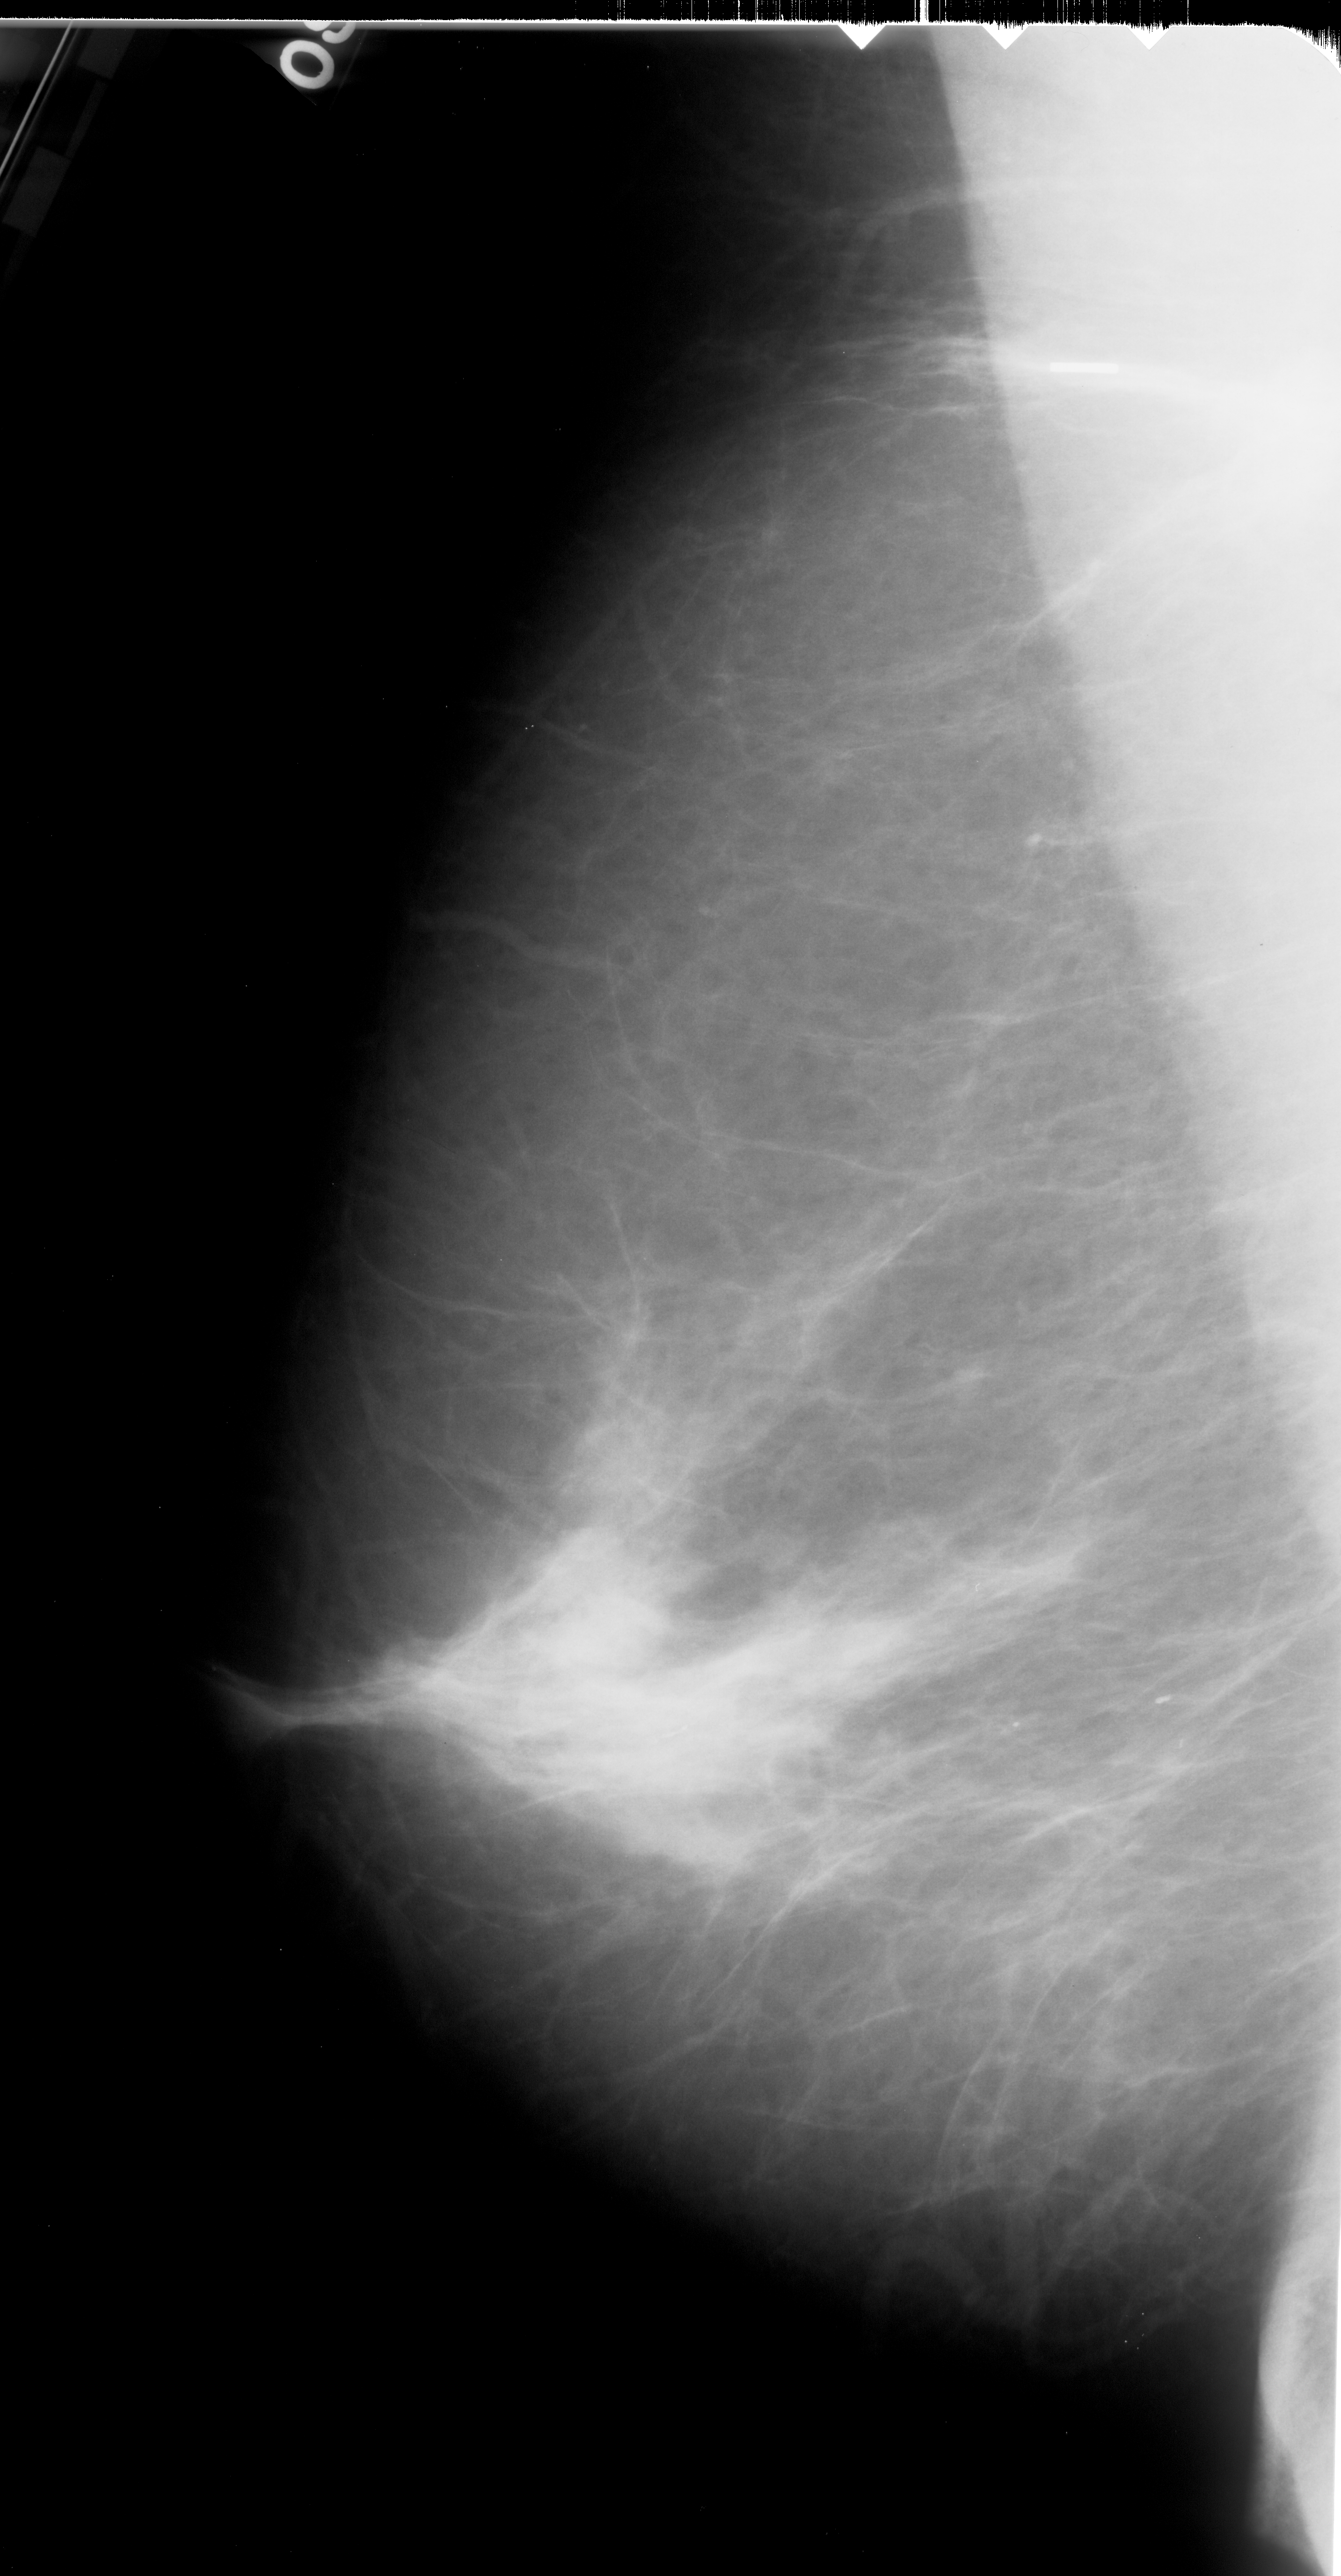
Mammogram (digitized film), left breast, MLO view, BI-RADS breast density category 2 (scale 1–4).
Finding: calcifications, morphology fine linear branching, distribution linear; BI-RADS assessment category 4; pathology result (as recorded, not read from the image): malignant.